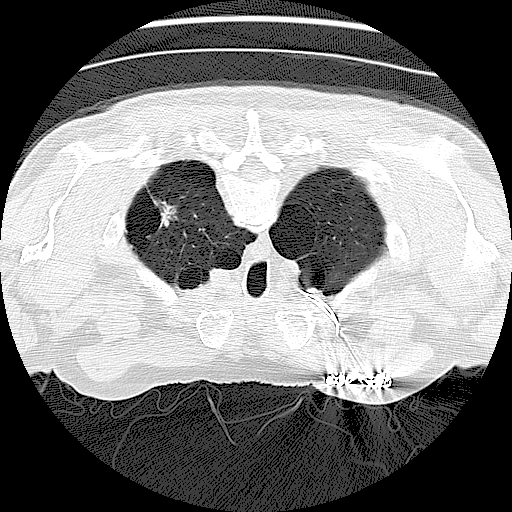
Low-dose screening chest CT, axial slice. Baseline annual screen. Lung window (W 1500 / L -600 HU). 2.5 mm slice thickness. Lung (sharp) reconstruction kernel (LUNG). 120 kVp. Slice 21 of 138 in the series. Male participant, aged 73 years at enrolment. Current smoker at enrolment.
• Lesion marked by an expert reader, bounding box <140,192,186,237> (left, top, right, bottom; pixels).
• The screening reader recorded 2 non-calcified nodules or masses ≥4 mm on this exam; which of them this box marks is not recorded.
• Lung cancer was diagnosed 308 days after this screen: neoplasm, malignant, stage IV (AJCC 6th edition).